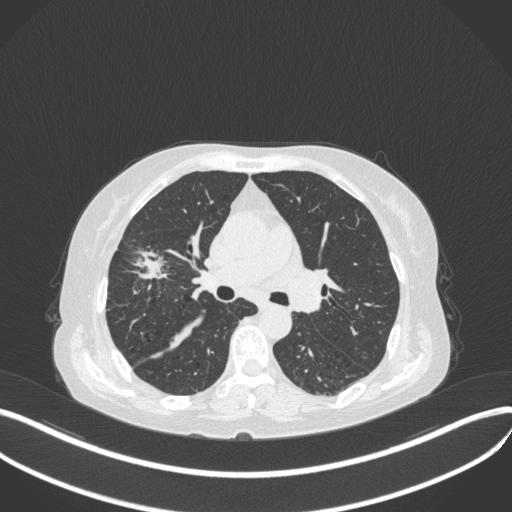
Chest CT, one axial slice. Slice 240 of 429 in the series (ordered by position). Reconstruction kernel B31f. Lung window (W 1500 / L -600 HU). 1 mm slice thickness. 512 × 512 image matrix. Female patient, age 69 years. From the clinical record (not read from this slice): clinical TNM (as recorded): T1b N3 M0.
Annotated regions visible in this slice (bounding box drawn by a radiologist):
- lung tumour (recorded histology: small cell carcinoma): bounding box [x1, y1, x2, y2] px = [124, 245, 176, 288]